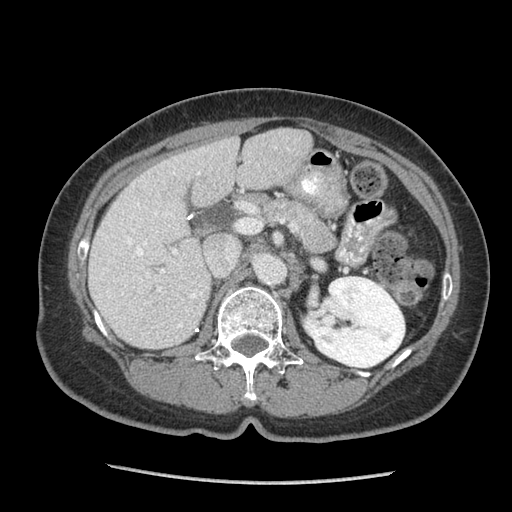
Contrast-enhanced abdominal CT (liver protocol), one axial slice. Position 41 of 105 along the scan axis. Reconstruction kernel STANDARD. 140 kVp. Soft-tissue window (W 400 / L 40 HU). 2.5 mm slice thickness. 512 × 512 image matrix. Case-level facts recorded for this patient, not image findings: diagnosis: hepatocellular carcinoma (patient treated with transarterial chemoembolisation; whether this scan precedes or follows treatment is not stated here); TNM stage (as recorded): Stage-I; Child-Pugh class: A; tumour differentiation: moderately differentiated; tumour nodularity: uninodular.
Annotated regions visible in this slice (semi-automatically segmented with operator editing):
- liver parenchyma outside the tumour (the mass and vessels are separate outlines, so this box may not span the whole liver): box from (x=88, y=128) to (x=312, y=348) px
- liver vessels: (x=107, y=172)–(x=202, y=328)